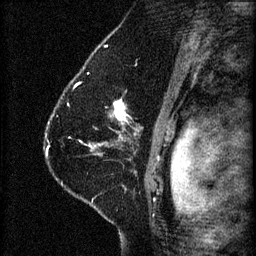
Breast MRI (dynamic contrast-enhanced), one sagittal slice. Slice 44 of 60 in the series (ordered by position). 3 images stored at this slice position (order not interpretable as contrast timing). 1.5 T. TE 4.2 ms, TR 8.2 ms. 256 × 256 image matrix. Patient: female, 41 years.
Annotated regions visible in this slice (semi-automatically segmented with operator editing):
- analysis volume of interest (the breast-tissue region the enhancement analysis was run in; not a lesion): bounding box [x1, y1, x2, y2] px = [68, 92, 165, 173]
- tumour enhancement mask (voxels above the 70 % enhancement threshold inside the analysis volume of interest): [89, 100, 128, 149]